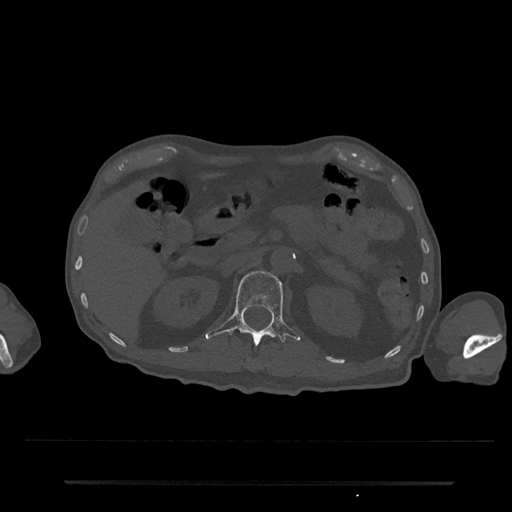
CT including the spine, one axial slice. Position 134 of 797 along the scan axis. Bone window (W 1800 / L 400 HU). 512 × 512 image matrix, field of view 427 × 427 mm. Male patient, age 74 years. From the clinical record (not read from this slice): primary cancer: prostate.
Annotated regions visible in this slice (semi-automatically segmented with operator editing):
- L1 vertebra: box from (x=205, y=271) to (x=301, y=345) px